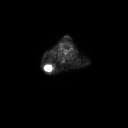
FDG PET of an extremity soft-tissue mass (from a PET/CT study), one axial slice. Position 221 of 267 along the scan axis. 128 × 128 image matrix. Male patient, age 61 years. From the clinical record (not read from this slice): histological type: pleiomorphic spindle cell undifferentiated; grade: high; site of the primary tumour: right parascapusular.
Annotated regions visible in this slice (expert contour drawn on MRI and transferred to this co-registered scan by the dataset authors):
- gross tumour volume including surrounding oedema: bounding box <45,65,54,71> (left, top, right, bottom; pixels)
- gross tumour volume (mass): <45,66,49,70>